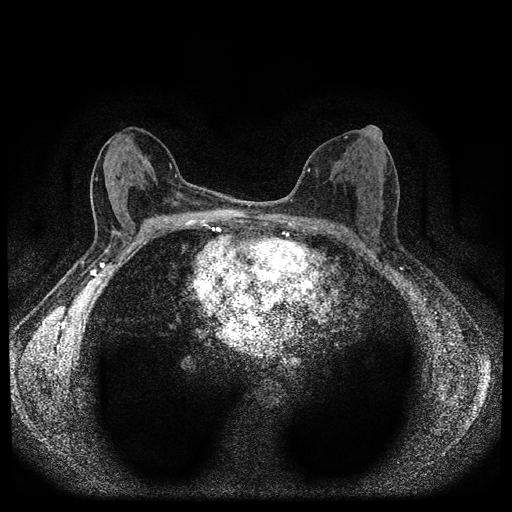
Breast MRI (dynamic contrast-enhanced, multi-phase), one axial slice. Position 49 of 112 along the scan axis. Dynamic contrast-enhanced series, time point 2 of 5 at this slice position (early post-contrast). 1.5 T. TE 2.7 ms, TR 5.4 ms. 2 mm slice thickness. 512 × 512 image matrix. Patient: female, 61 years.
Structures marked on this image (semi-automatic segmentation, software-assisted and operator-edited):
- breast lesion (labelled 'tumour' in the annotation; benign lesions carry a separate 'benign' label): bounding box <170,192,182,208> (left, top, right, bottom; pixels)